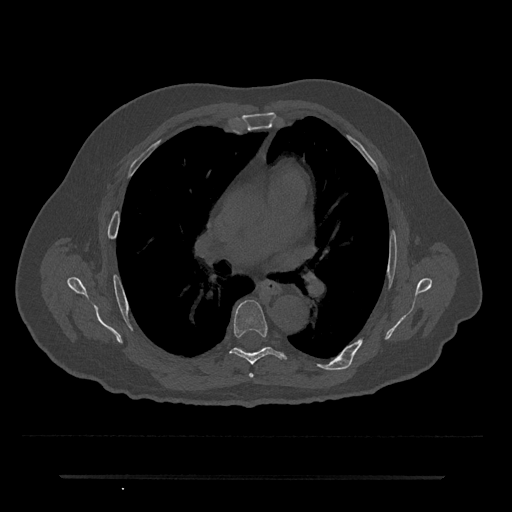
CT including the spine, one axial slice; reconstruction kernel Br40s/3; bone window (W 1800 / L 400 HU); 0.5 mm slice thickness; 512 × 512 image matrix. Male patient, age 69 years. From the clinical record (not read from this slice): primary cancer: prostate.
Annotated regions visible in this slice (semi-automatically segmented with operator editing):
- T5 vertebra: bounding box <249,373,254,378> (left, top, right, bottom; pixels)
- T6 vertebra: <230,300,285,365>